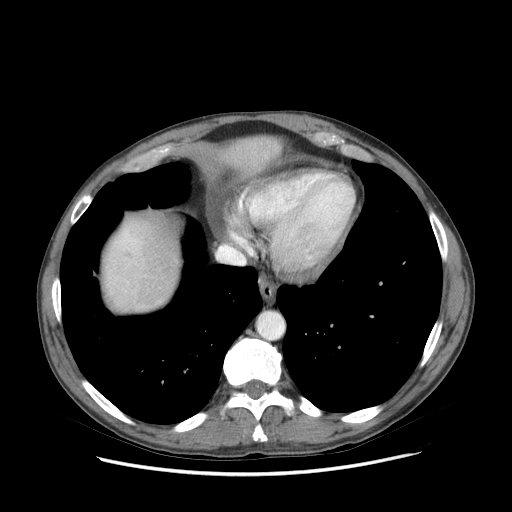
Contrast-enhanced abdominal CT (liver protocol), one axial slice; slice 74 of 89 in the series (ordered by position); reconstruction kernel STANDARD; soft-tissue window (W 400 / L 40 HU); 2.5 mm slice thickness; 512 × 512 image matrix, field of view 380 × 380 mm. Case-level facts recorded for this patient, not image findings: diagnosis: hepatocellular carcinoma (patient treated with transarterial chemoembolisation; whether this scan precedes or follows treatment is not stated here); TNM stage (as recorded): Stage-IIIB; Child-Pugh class: A; tumour differentiation: moderately differentiated; tumour nodularity: multinodular.
Outlined on this slice (semi-automatic segmentation, software-assisted and operator-edited):
- liver parenchyma outside the tumour (the mass and vessels are separate outlines, so this box may not span the whole liver): bounding box [x1, y1, x2, y2] px = [104, 136, 280, 310]
- liver vessels: [110, 229, 142, 285]